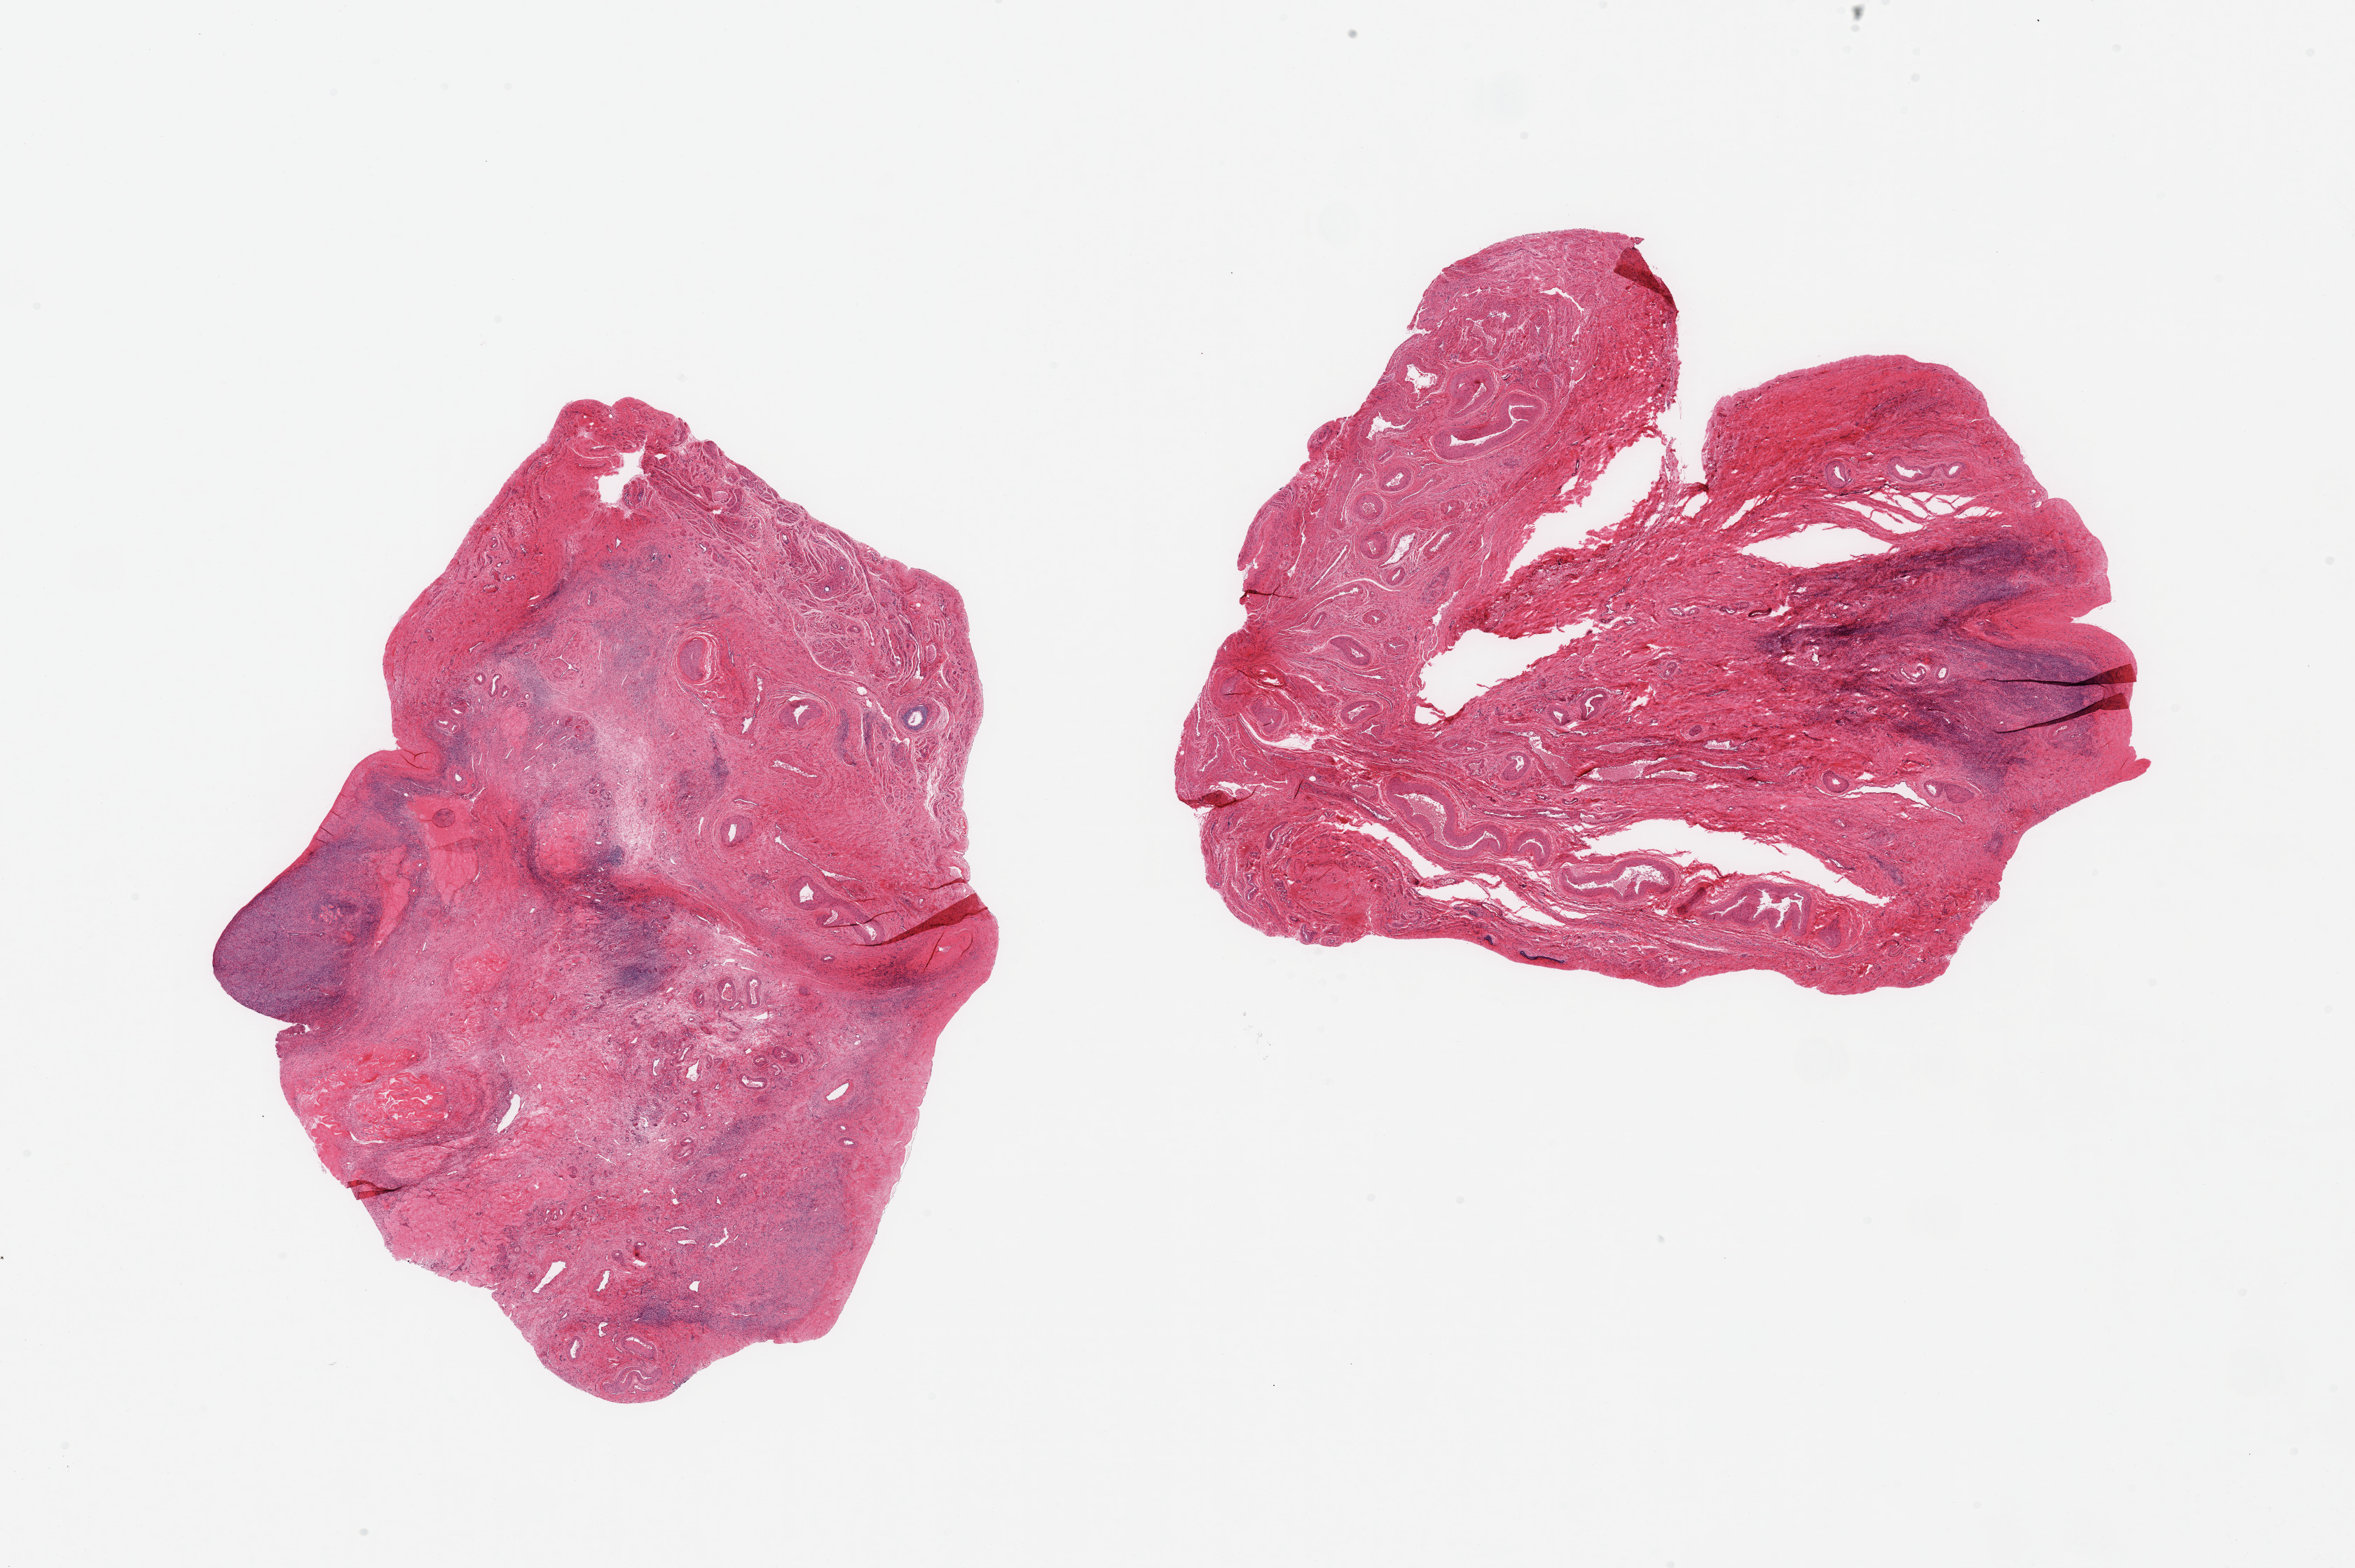
H&E whole-slide image, shown as a low-resolution overview of the whole scanned area (about 26.6 x 17.7 mm, slide scanned at 20x); PAXgene-fixed paraffin-embedded (PFPE) section; sampled site (target tissue): ovary; donor tissue sample. Donor sex: female.
Pathologist's review note for this sample: 2 pieces; atrophic; ovarian parenchyma comprises 20%.